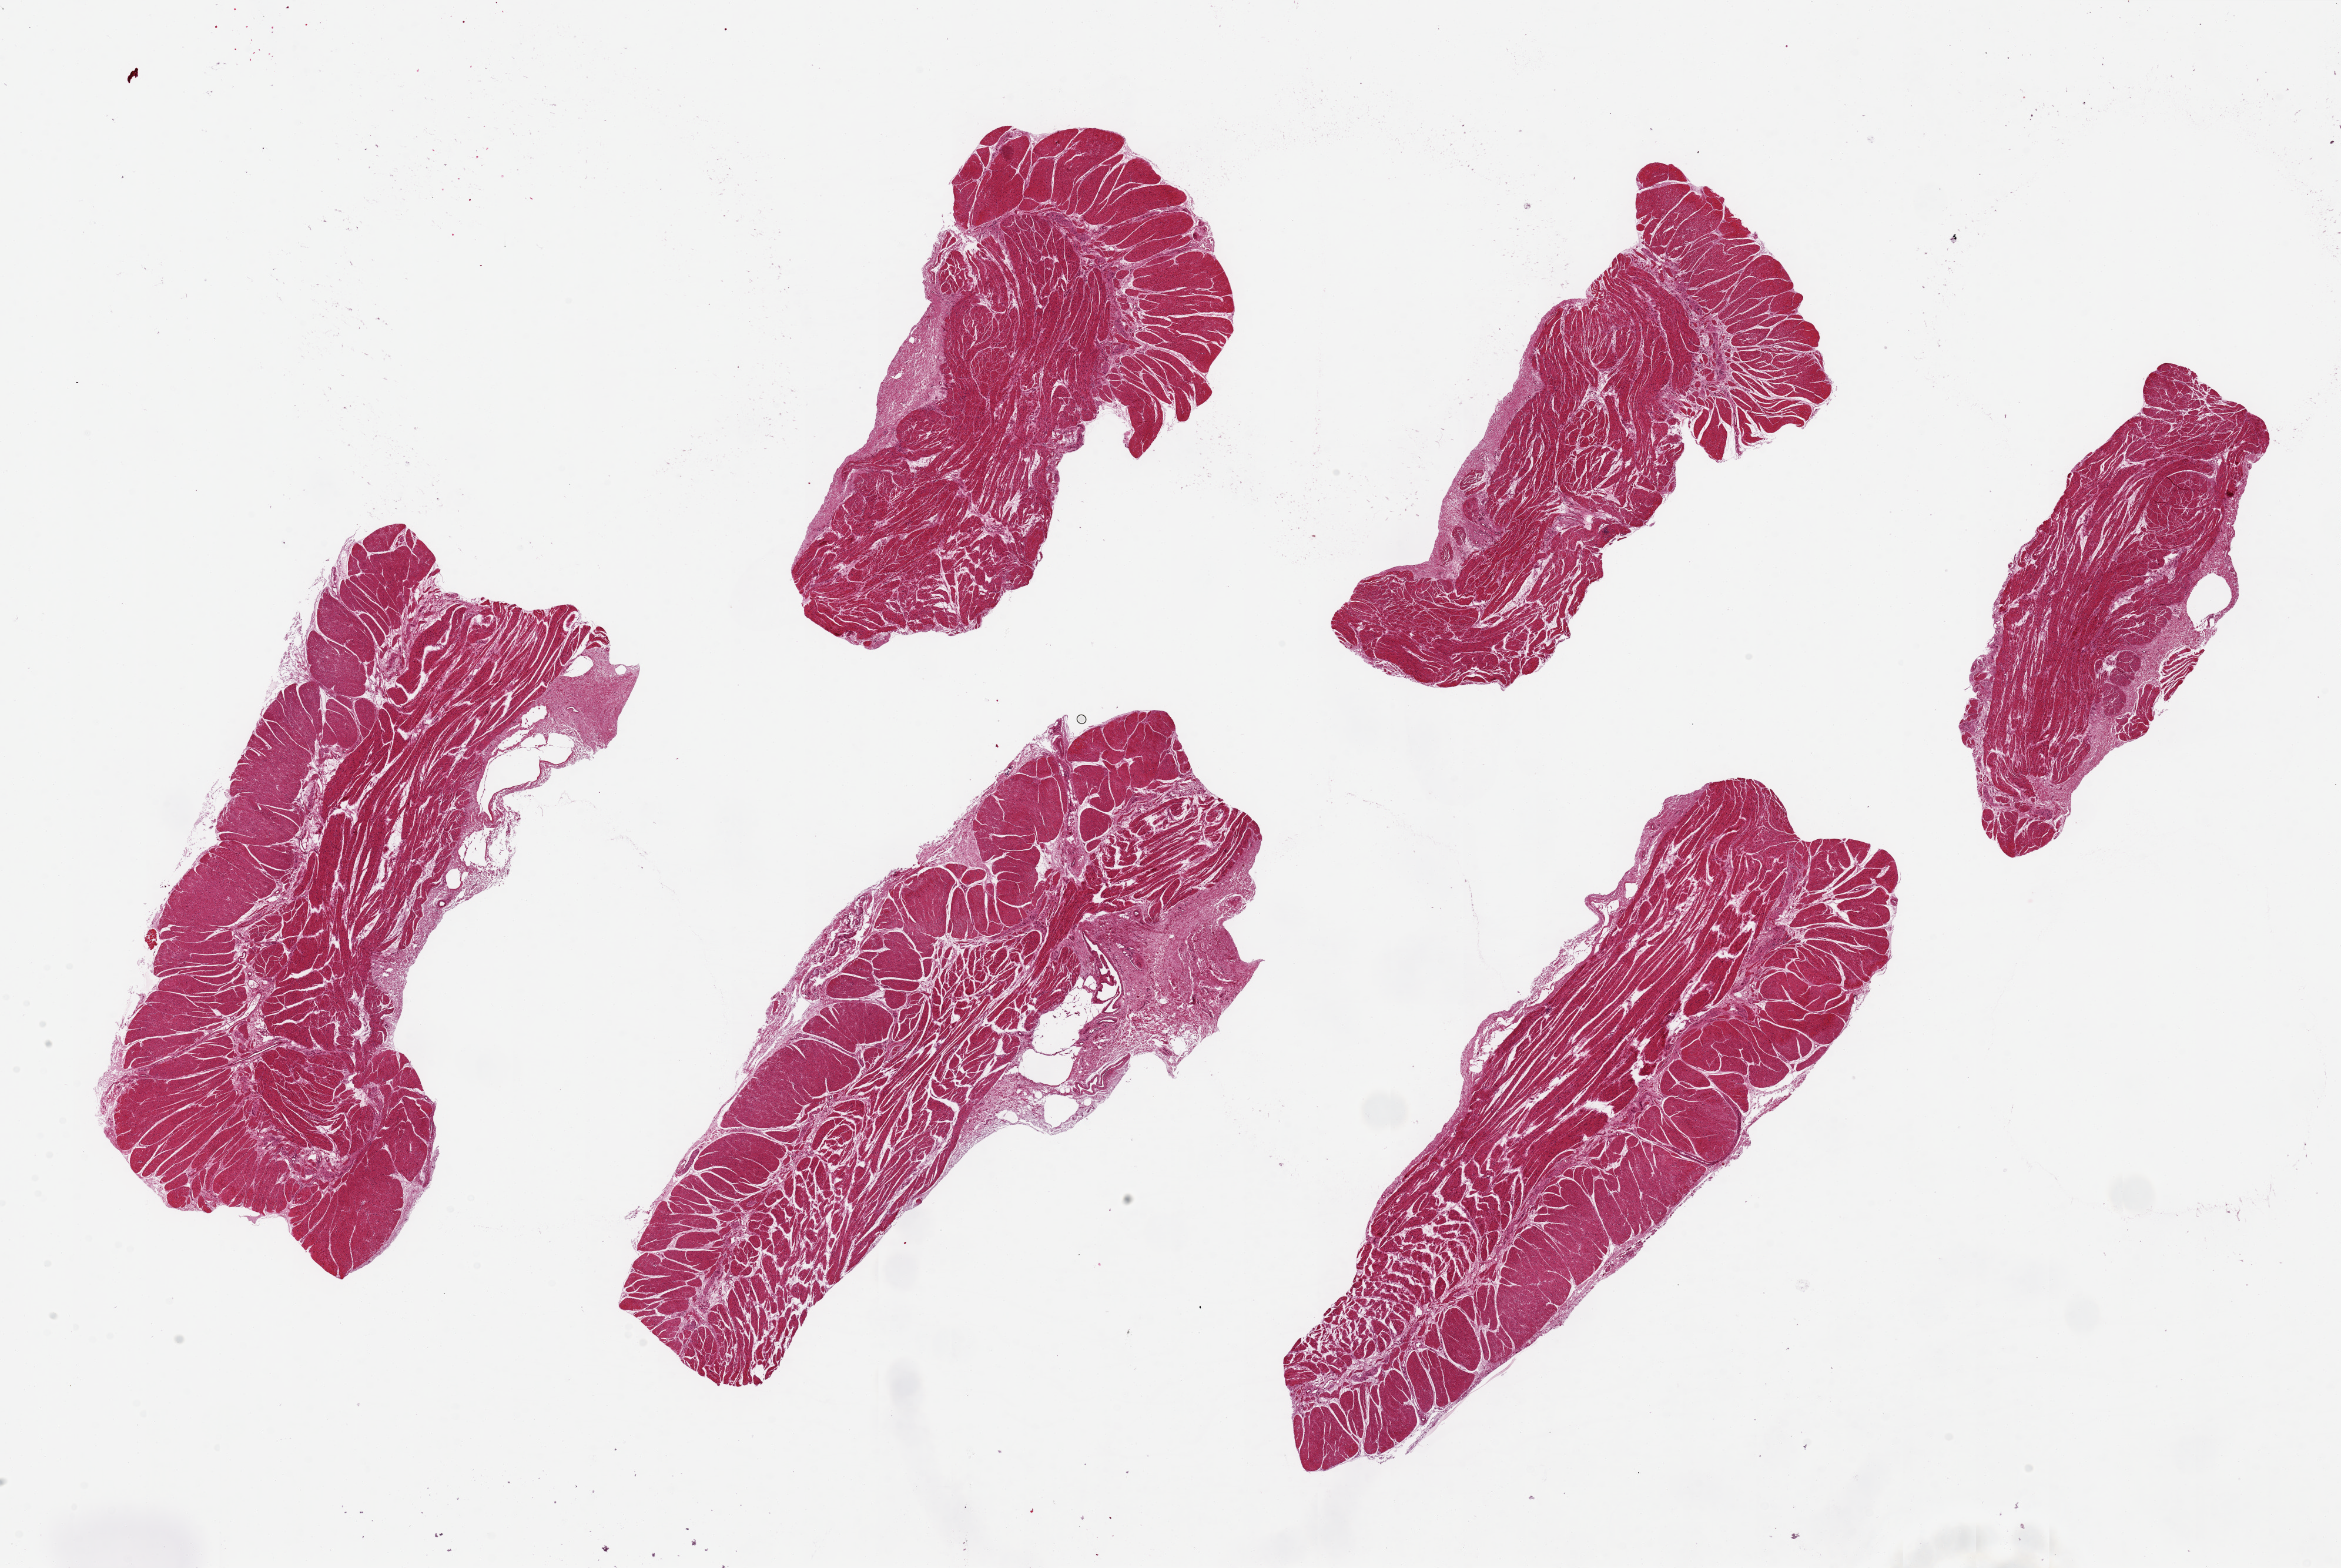
Digitized hematoxylin and eosin (H&E)-stained section — whole scanned area (about 31.5 x 21.1 mm) shown as a low-resolution overview. PAXgene-fixed, paraffin-embedded tissue. Target tissue: esophageal muscle. Tissue donor sample. Donor: male.
- reviewer comment on this tissue sample: 6 pieces, up to 11.3x3.5 mm; muscle with focal submucosa